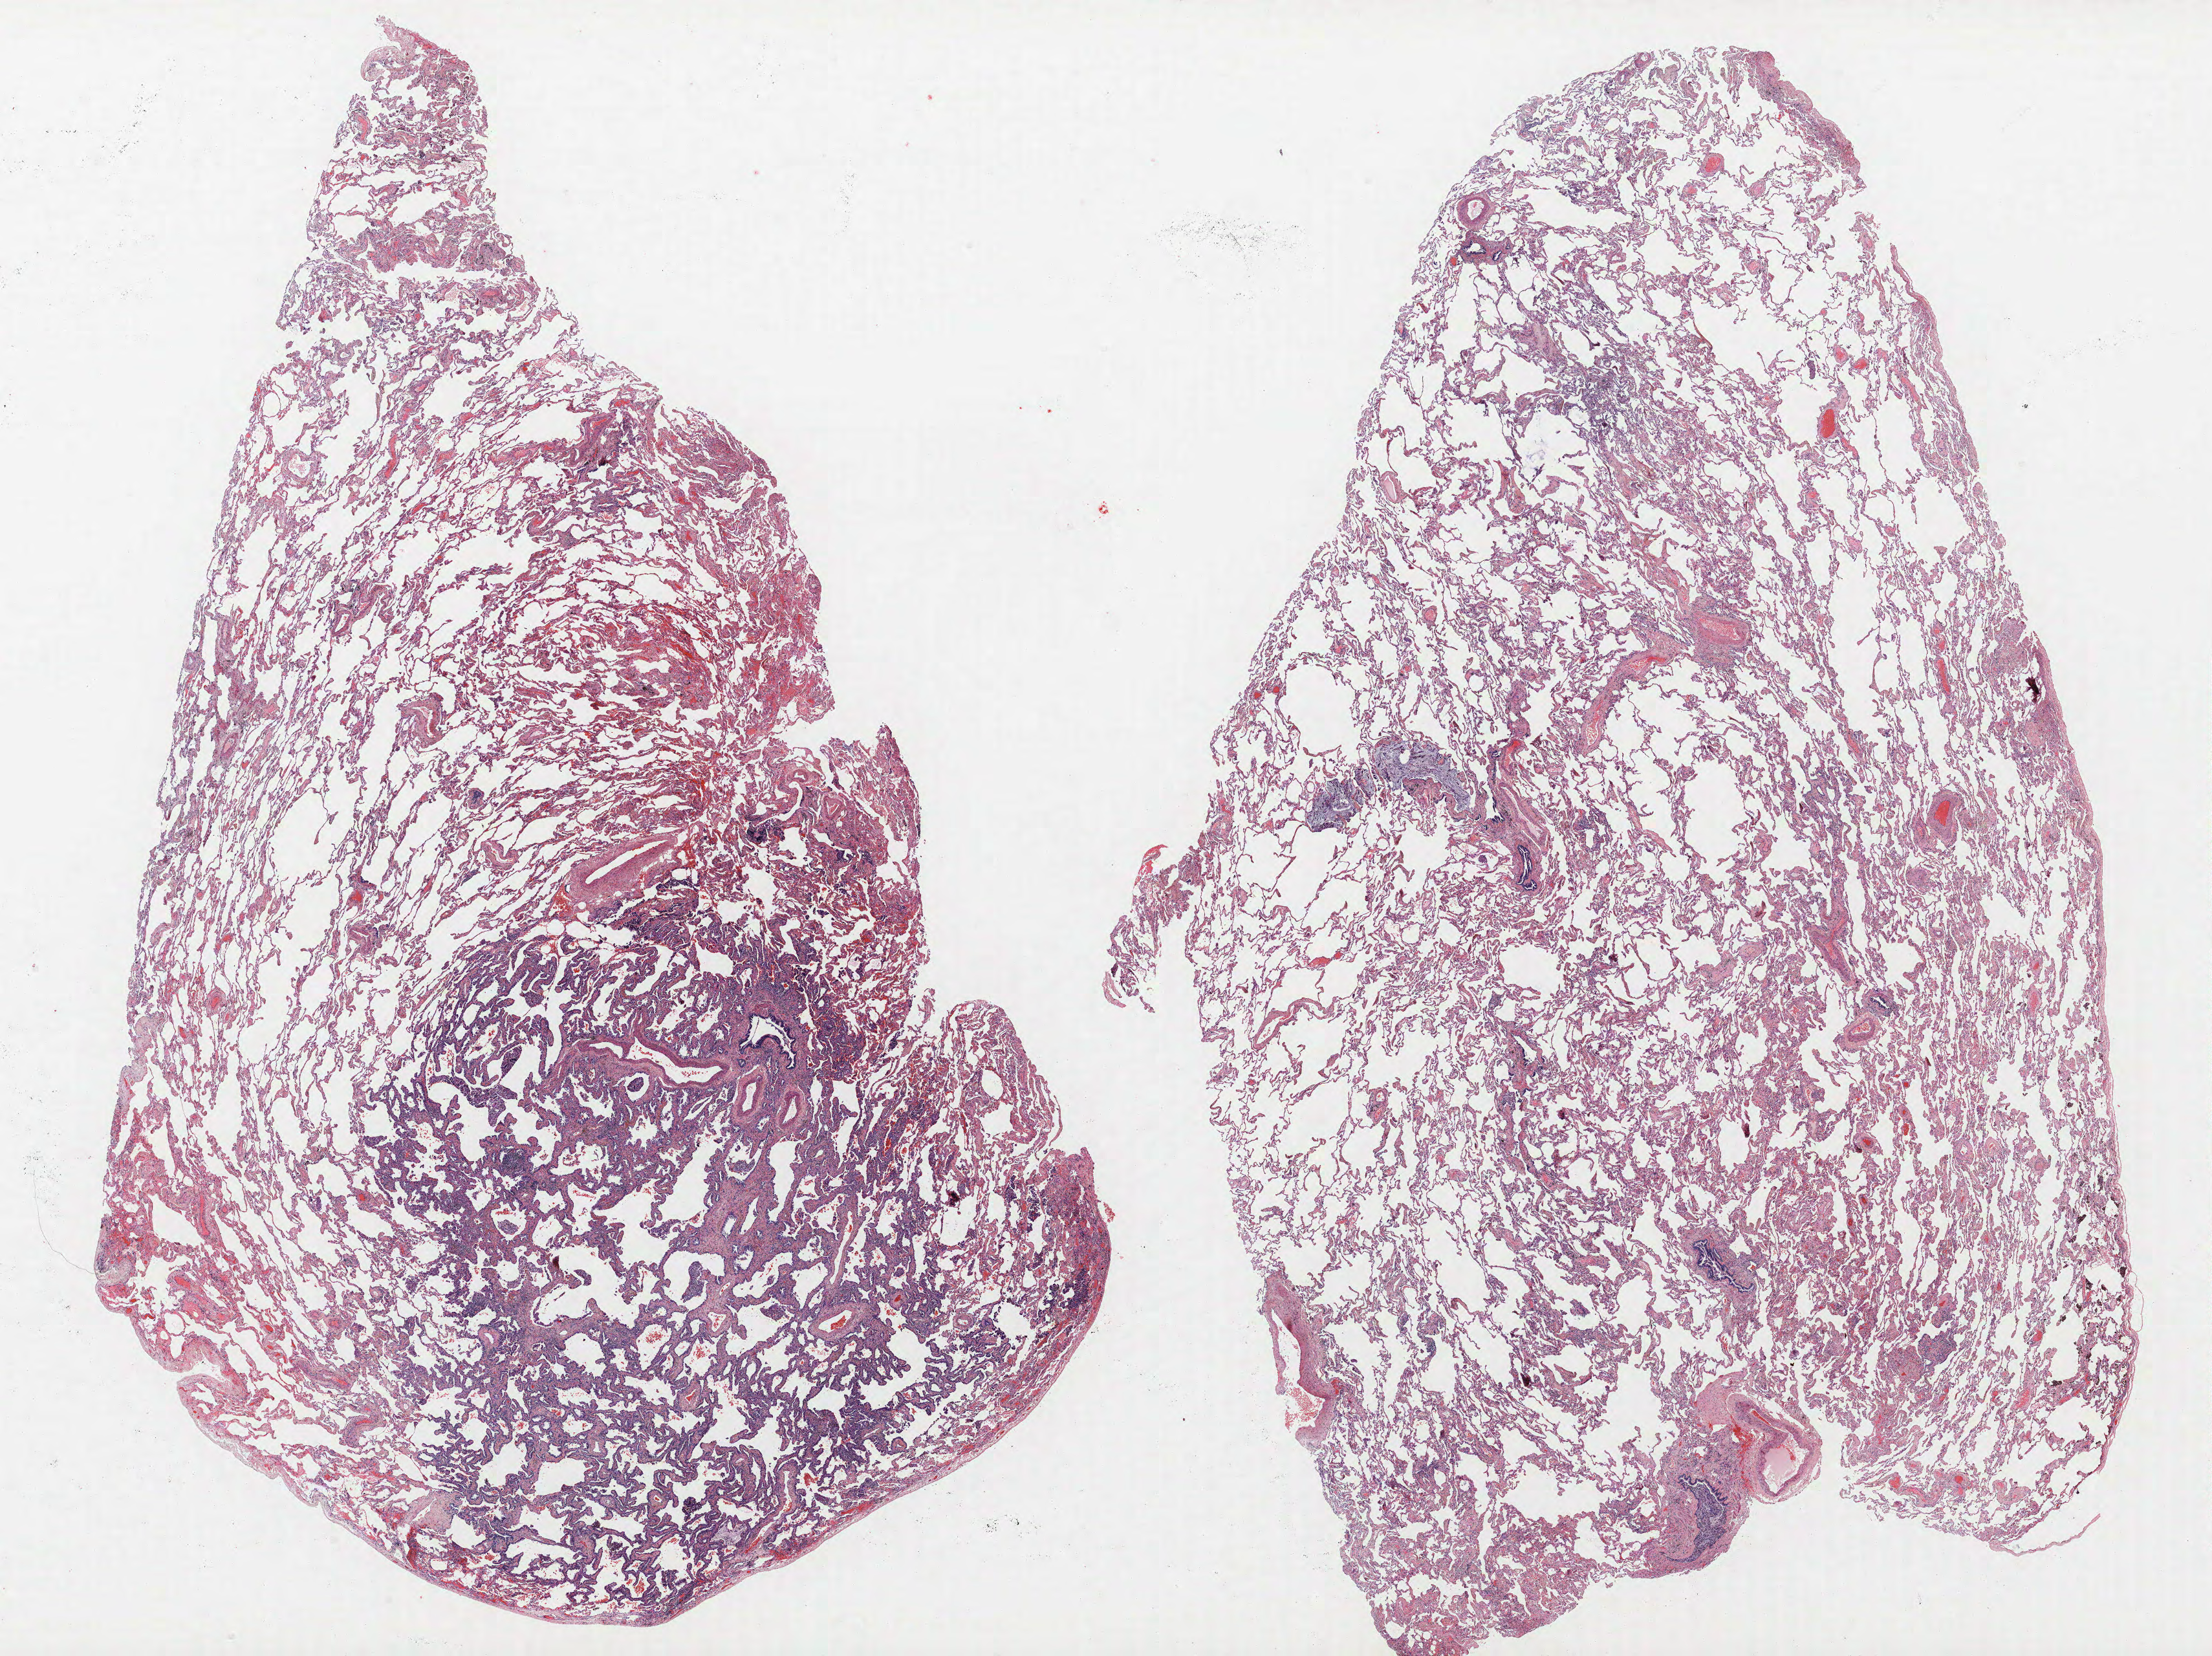
H&E-stained whole-slide image — a low-resolution overview of the entire scanned area, about 27.4 x 20.5 mm, formalin-fixed paraffin-embedded (FFPE) section, lung. Female, age 64 at enrolment. Former smoker at enrolment. Grade: well differentiated (G1).
- primary tumour location (clinical record): right upper lobe
- participant's lung-cancer diagnosis: Bronchiolo-alveolar adenocarcinoma, NOS (ICD-O-3 8250/3)
- stage (AJCC 6th edition): IA
- tumour size (pathology): 10 mm